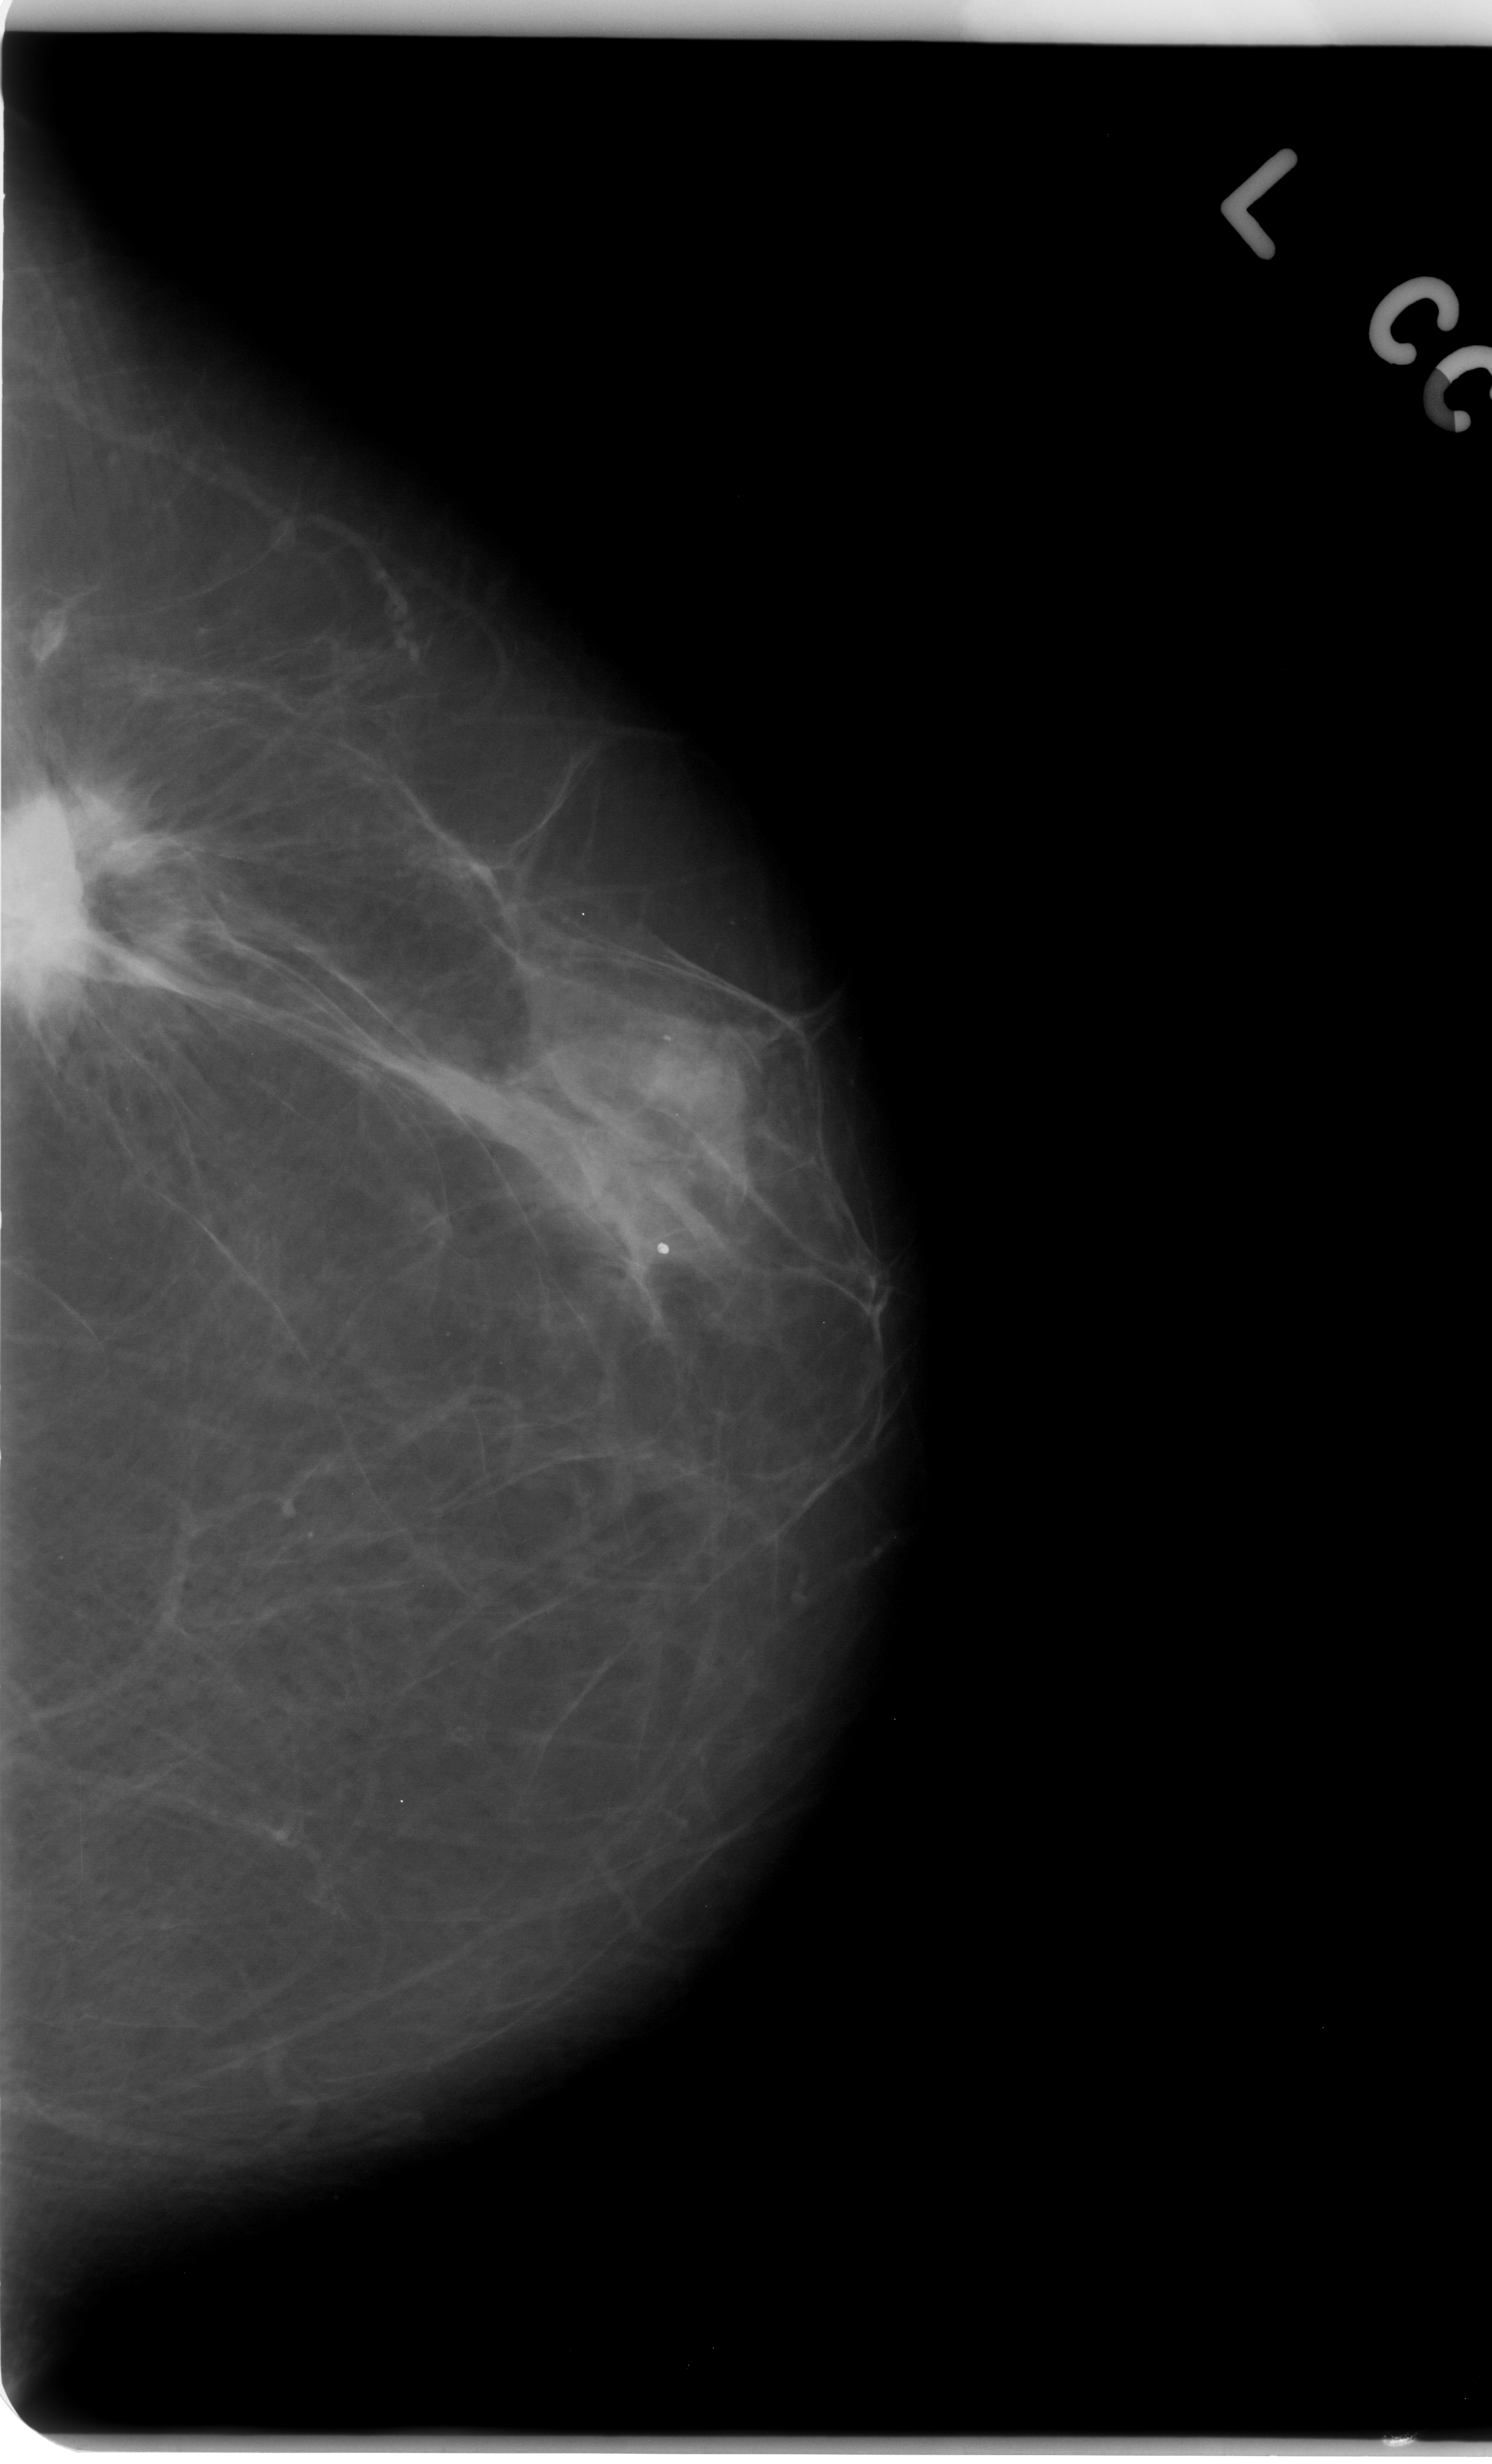
Digitized screen-film mammogram; left breast; CC view; breast composition: almost entirely fatty (BI-RADS density category 1 of 4); 1492 × 2464 image matrix.
Marked abnormalities (boxes around the expert regions of interest):
- mass, shape irregular, margins spiculated; BI-RADS assessment category 5; pathology result (as recorded, not read from the image): malignant: bounding box [x1, y1, x2, y2] px = [0, 719, 117, 1092]